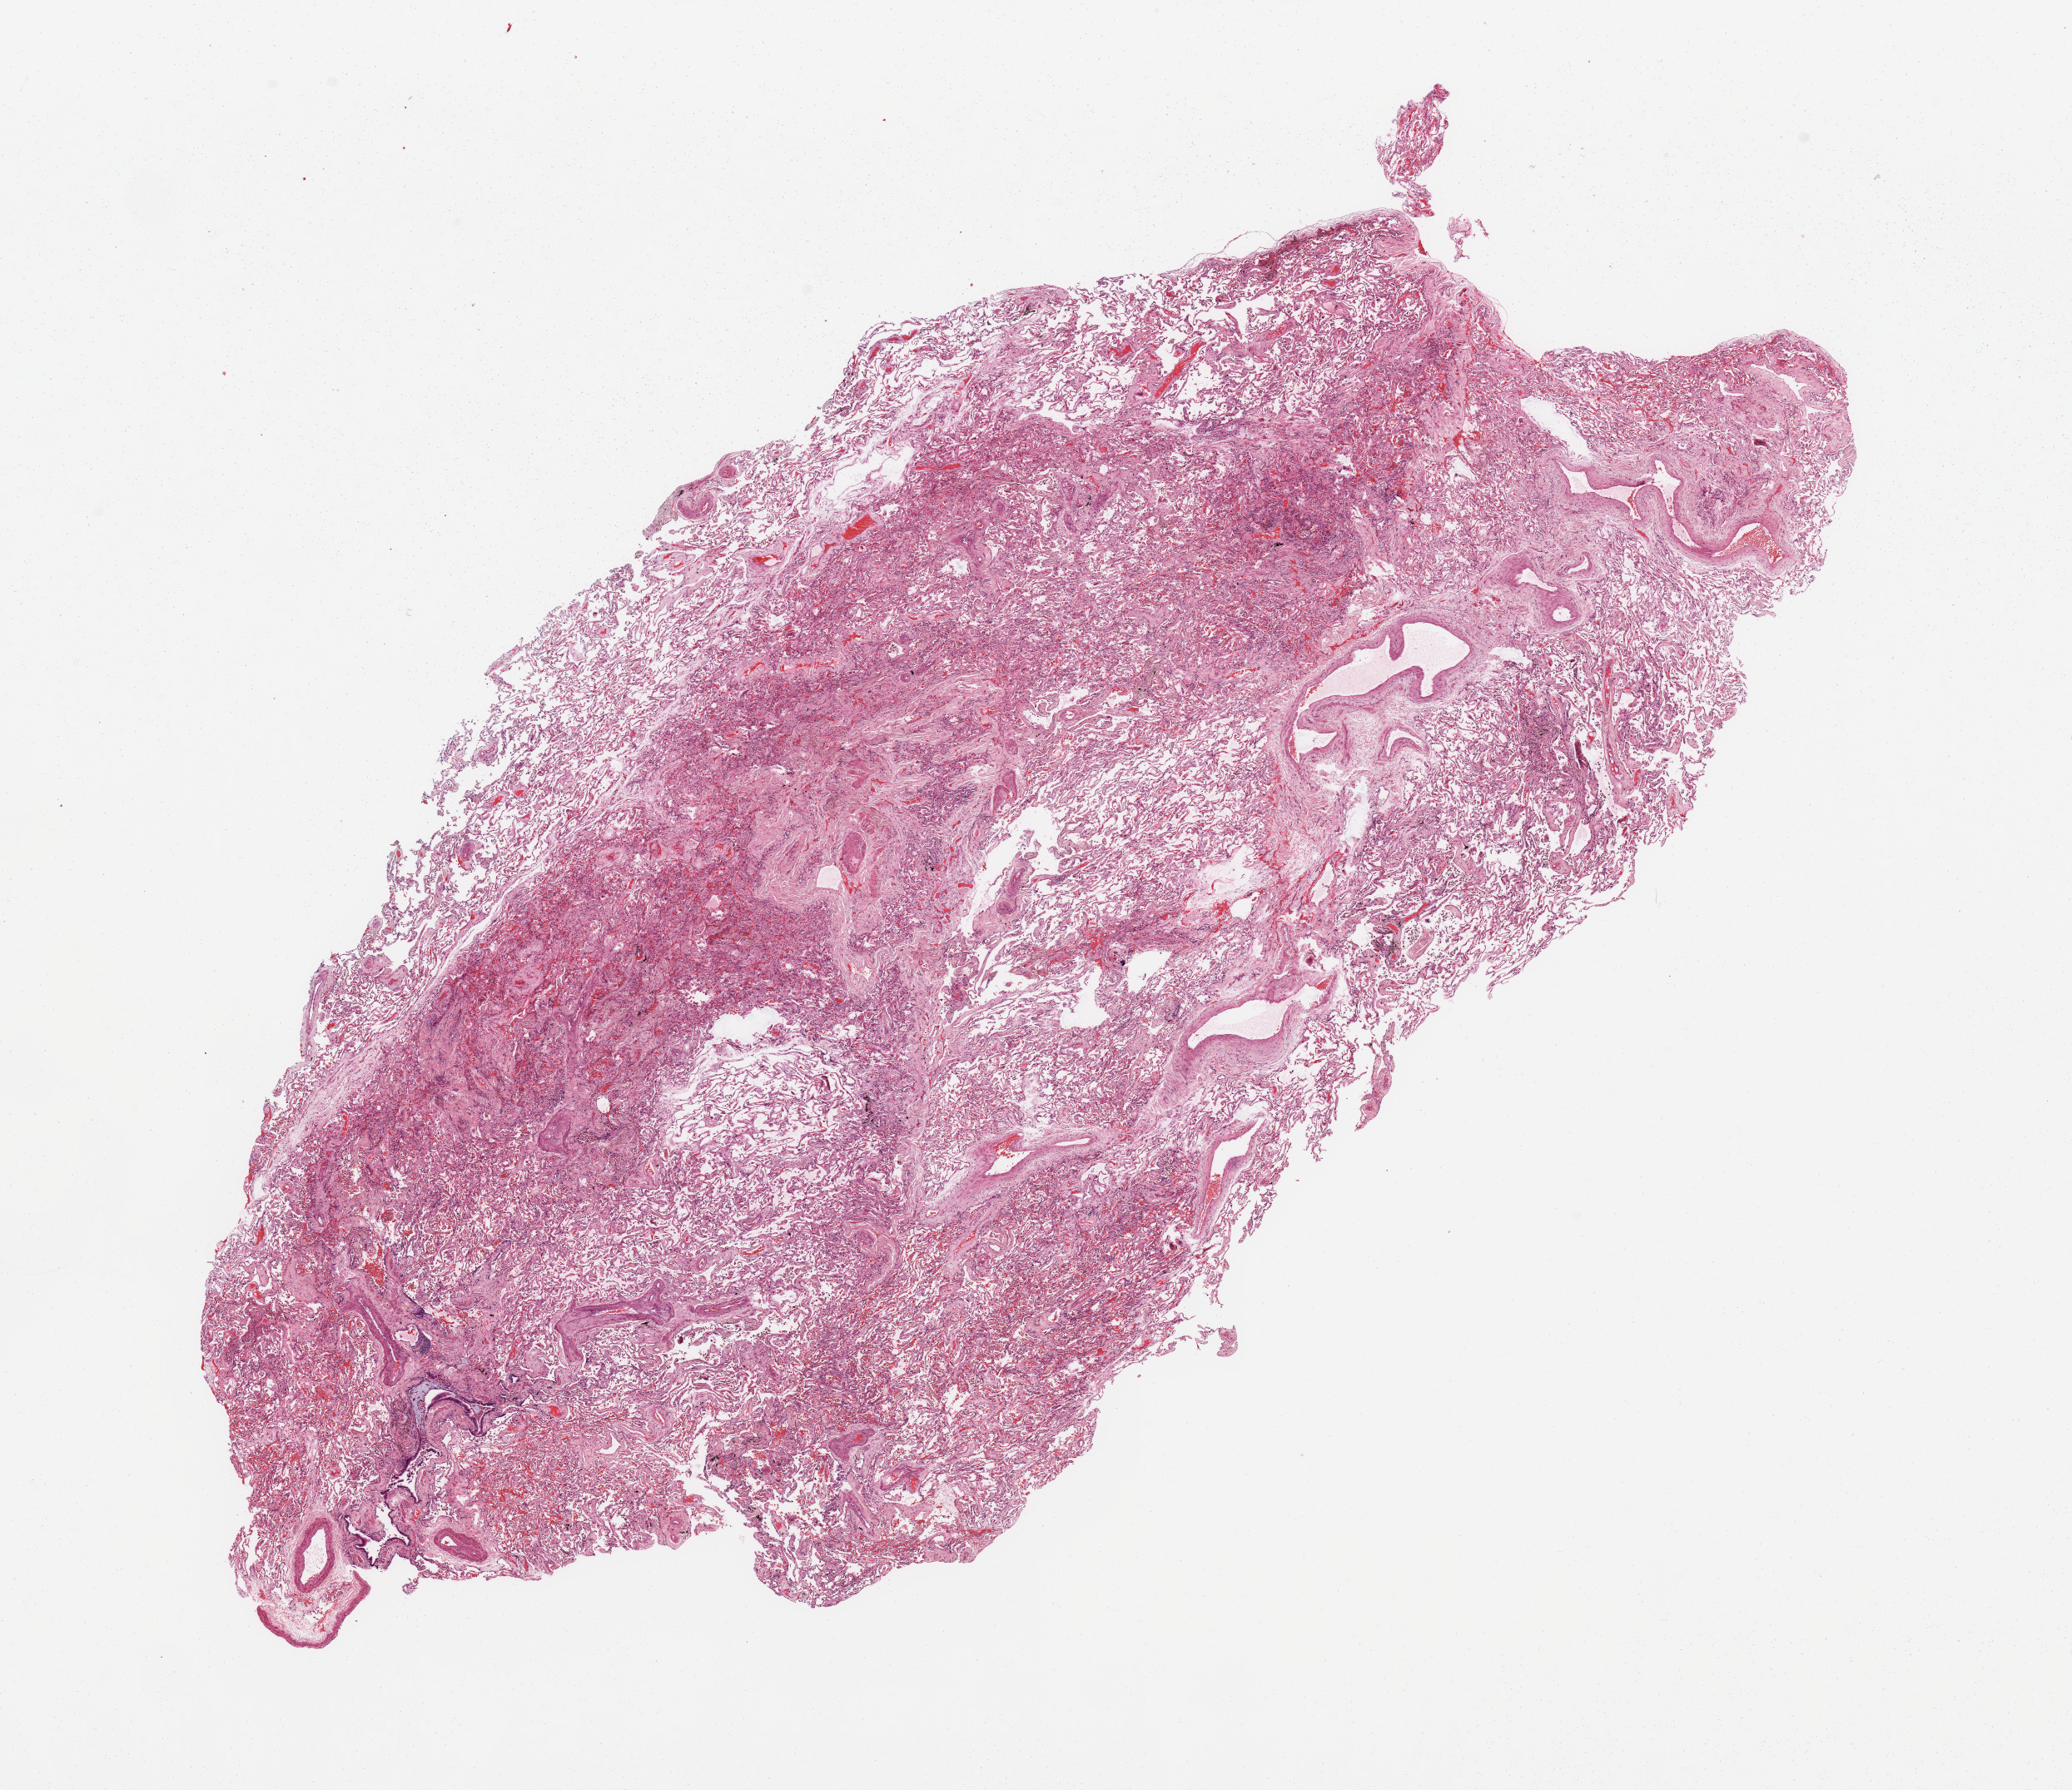
Whole-slide histology image, Hematoxylin and eosin (H&E) stained, a low-resolution overview of the entire scanned area, about 19.7 x 17.0 mm. Normal (non-tumour) tissue sample, sampled site: lung. 81-year-old female patient.
This section: normal (non-tumour) tissue from the same patient. Patient diagnosis: Squamous cell carcinoma, NOS.